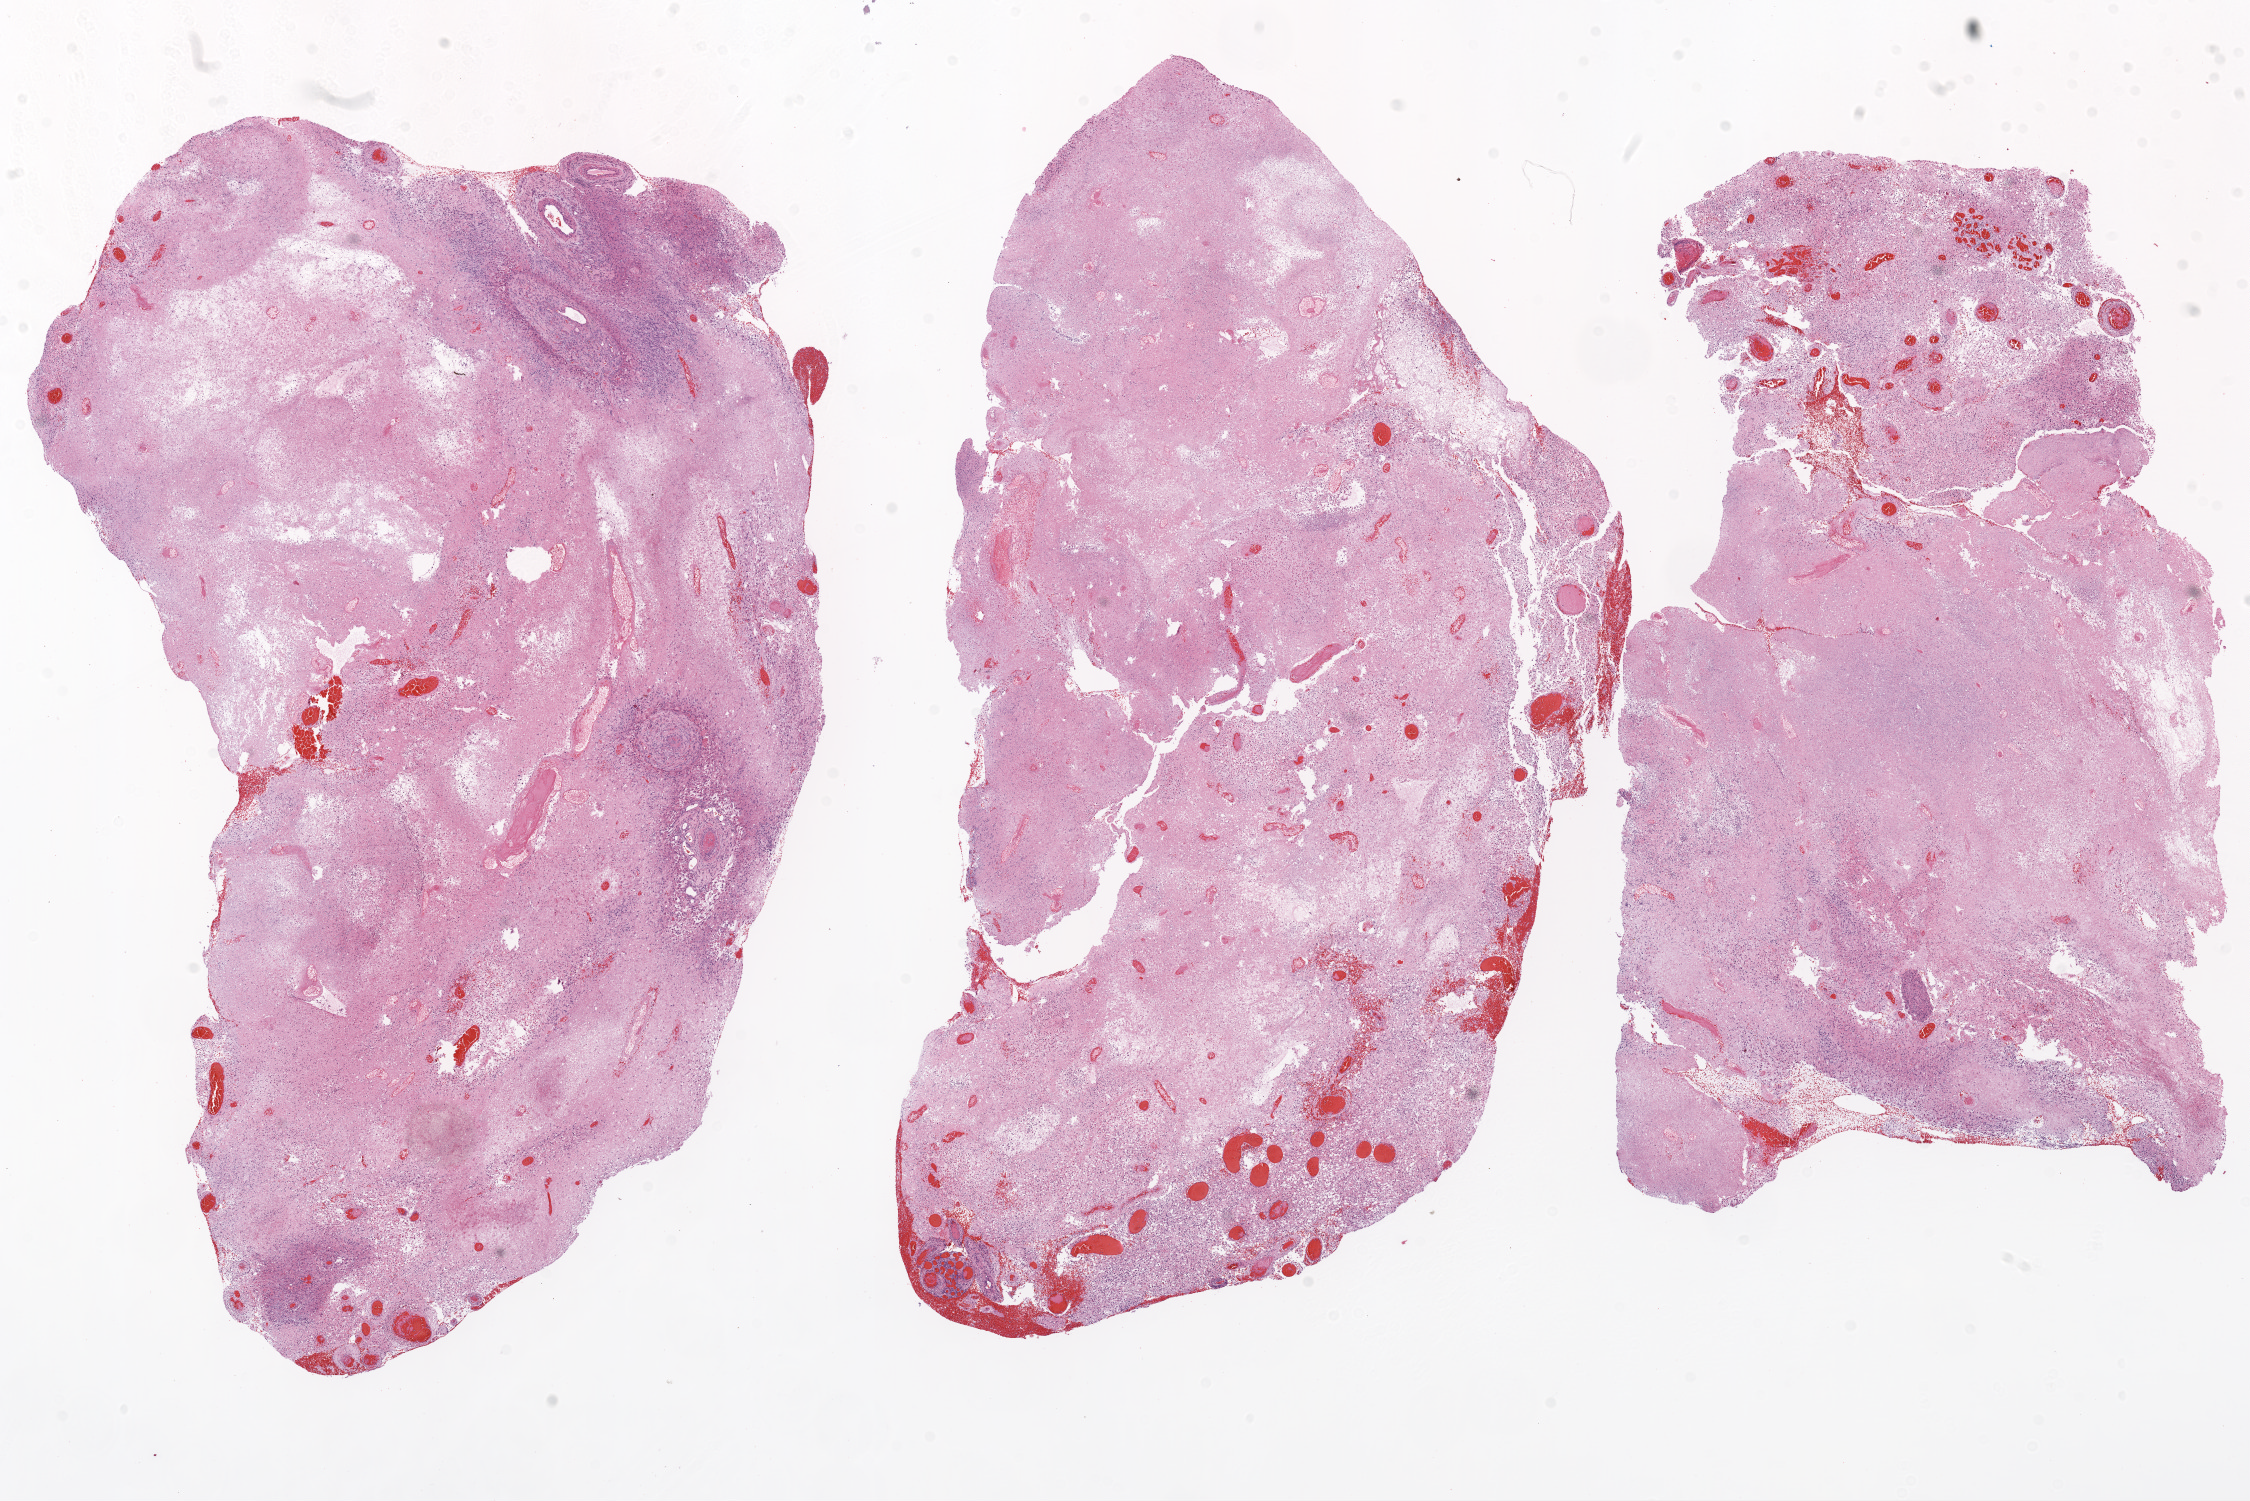
Digitized H&E tissue section (whole slide) — low-resolution overview of the scanned area, about 18.1 x 12.0 mm (acquisition: 20x scan), formalin-fixed paraffin-embedded (FFPE) diagnostic section, sample: primary tumour, brain. Male patient; age at initial diagnosis 58 years.
• diagnosis: Glioblastoma